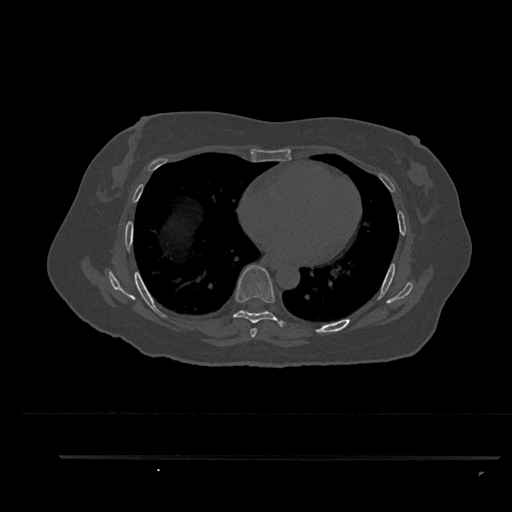
CT including the spine, one axial slice; slice 507 of 797 in the series (ordered by position); reconstruction kernel Br40s/3; 120 kVp; bone window (W 1800 / L 400 HU); 0.5 mm slice thickness; 512 × 512 image matrix. Patient: female, 44 years. Case-level facts recorded for this patient, not image findings: primary cancer: renal; vertebrae with lytic lesions (as recorded): L1.
Structures marked on this image (semi-automatic segmentation, software-assisted and operator-edited):
- T6 vertebra: bounding box [x1, y1, x2, y2] px = [250, 328, 257, 338]
- T7 vertebra: [232, 265, 286, 328]